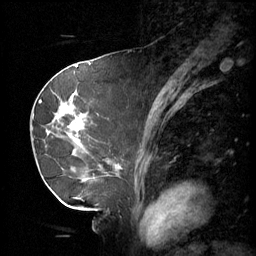
Breast MRI (dynamic contrast-enhanced), one sagittal slice; slice 27 of 60 in the series (ordered by position); 3 images stored at this slice position (order not interpretable as contrast timing); 1.5 T; TE 4.2 ms, TR 11 ms; 2 mm slice thickness; 256 × 256 image matrix, field of view 220 × 220 mm. Patient: female, 69 years.
Annotated regions visible in this slice (semi-automatic segmentation, software-assisted and operator-edited):
- analysis volume of interest (the breast-tissue region the enhancement analysis was run in; not a lesion): box from (x=36, y=88) to (x=116, y=189) px
- tumour enhancement mask (voxels above the 70 % enhancement threshold inside the analysis volume of interest): (x=57, y=104)–(x=116, y=183)